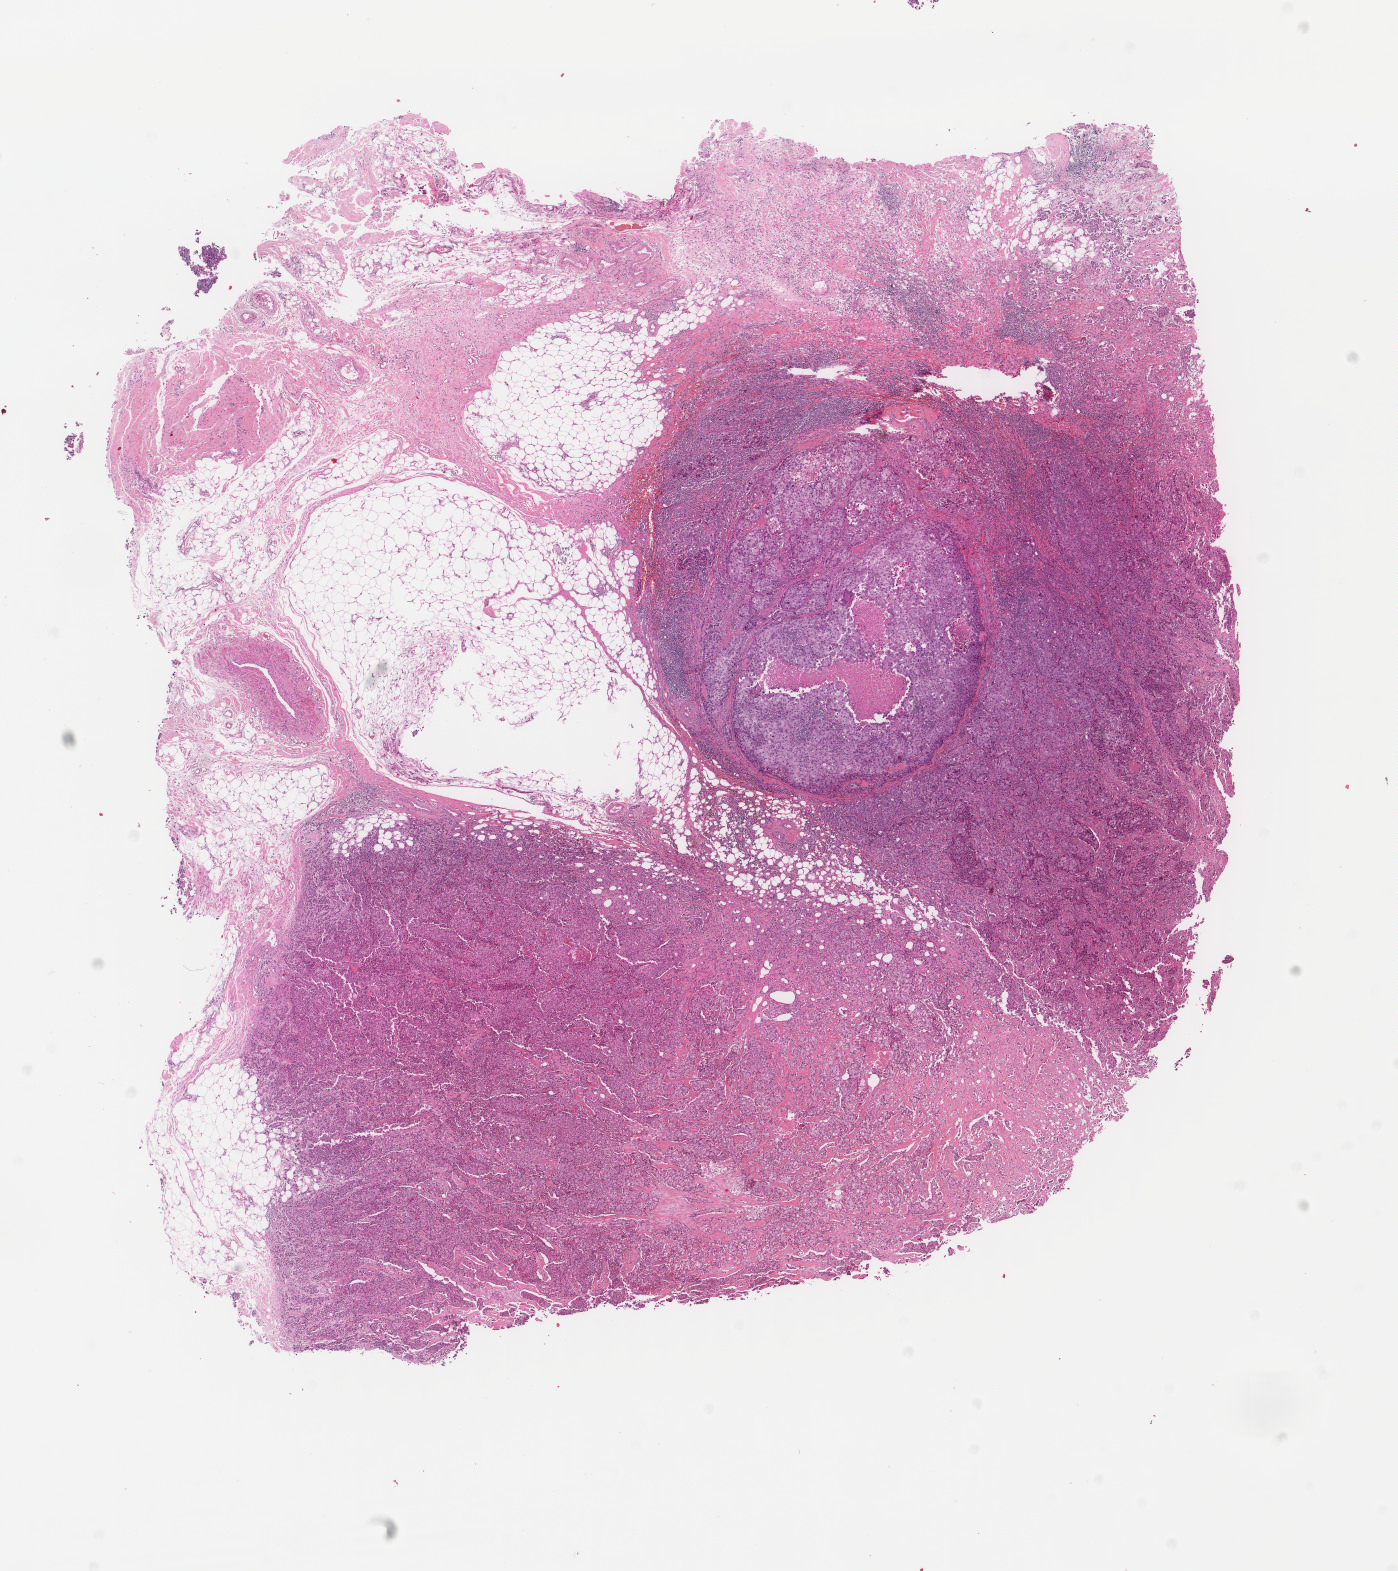
Whole-slide histology image, Hematoxylin and eosin (H&E) stained, whole scanned area (about 11.1 x 12.5 mm, slide scanned at 40x) shown as a low-resolution overview. Formalin-fixed paraffin-embedded (FFPE) diagnostic section. Primary tumour sample from the breast. Patient: female, age at initial diagnosis 56 years.
Histologic diagnosis: Infiltrating duct carcinoma, NOS. Laterality: left. TNM: T2 N0 M0. AJCC pathologic stage: IIA.